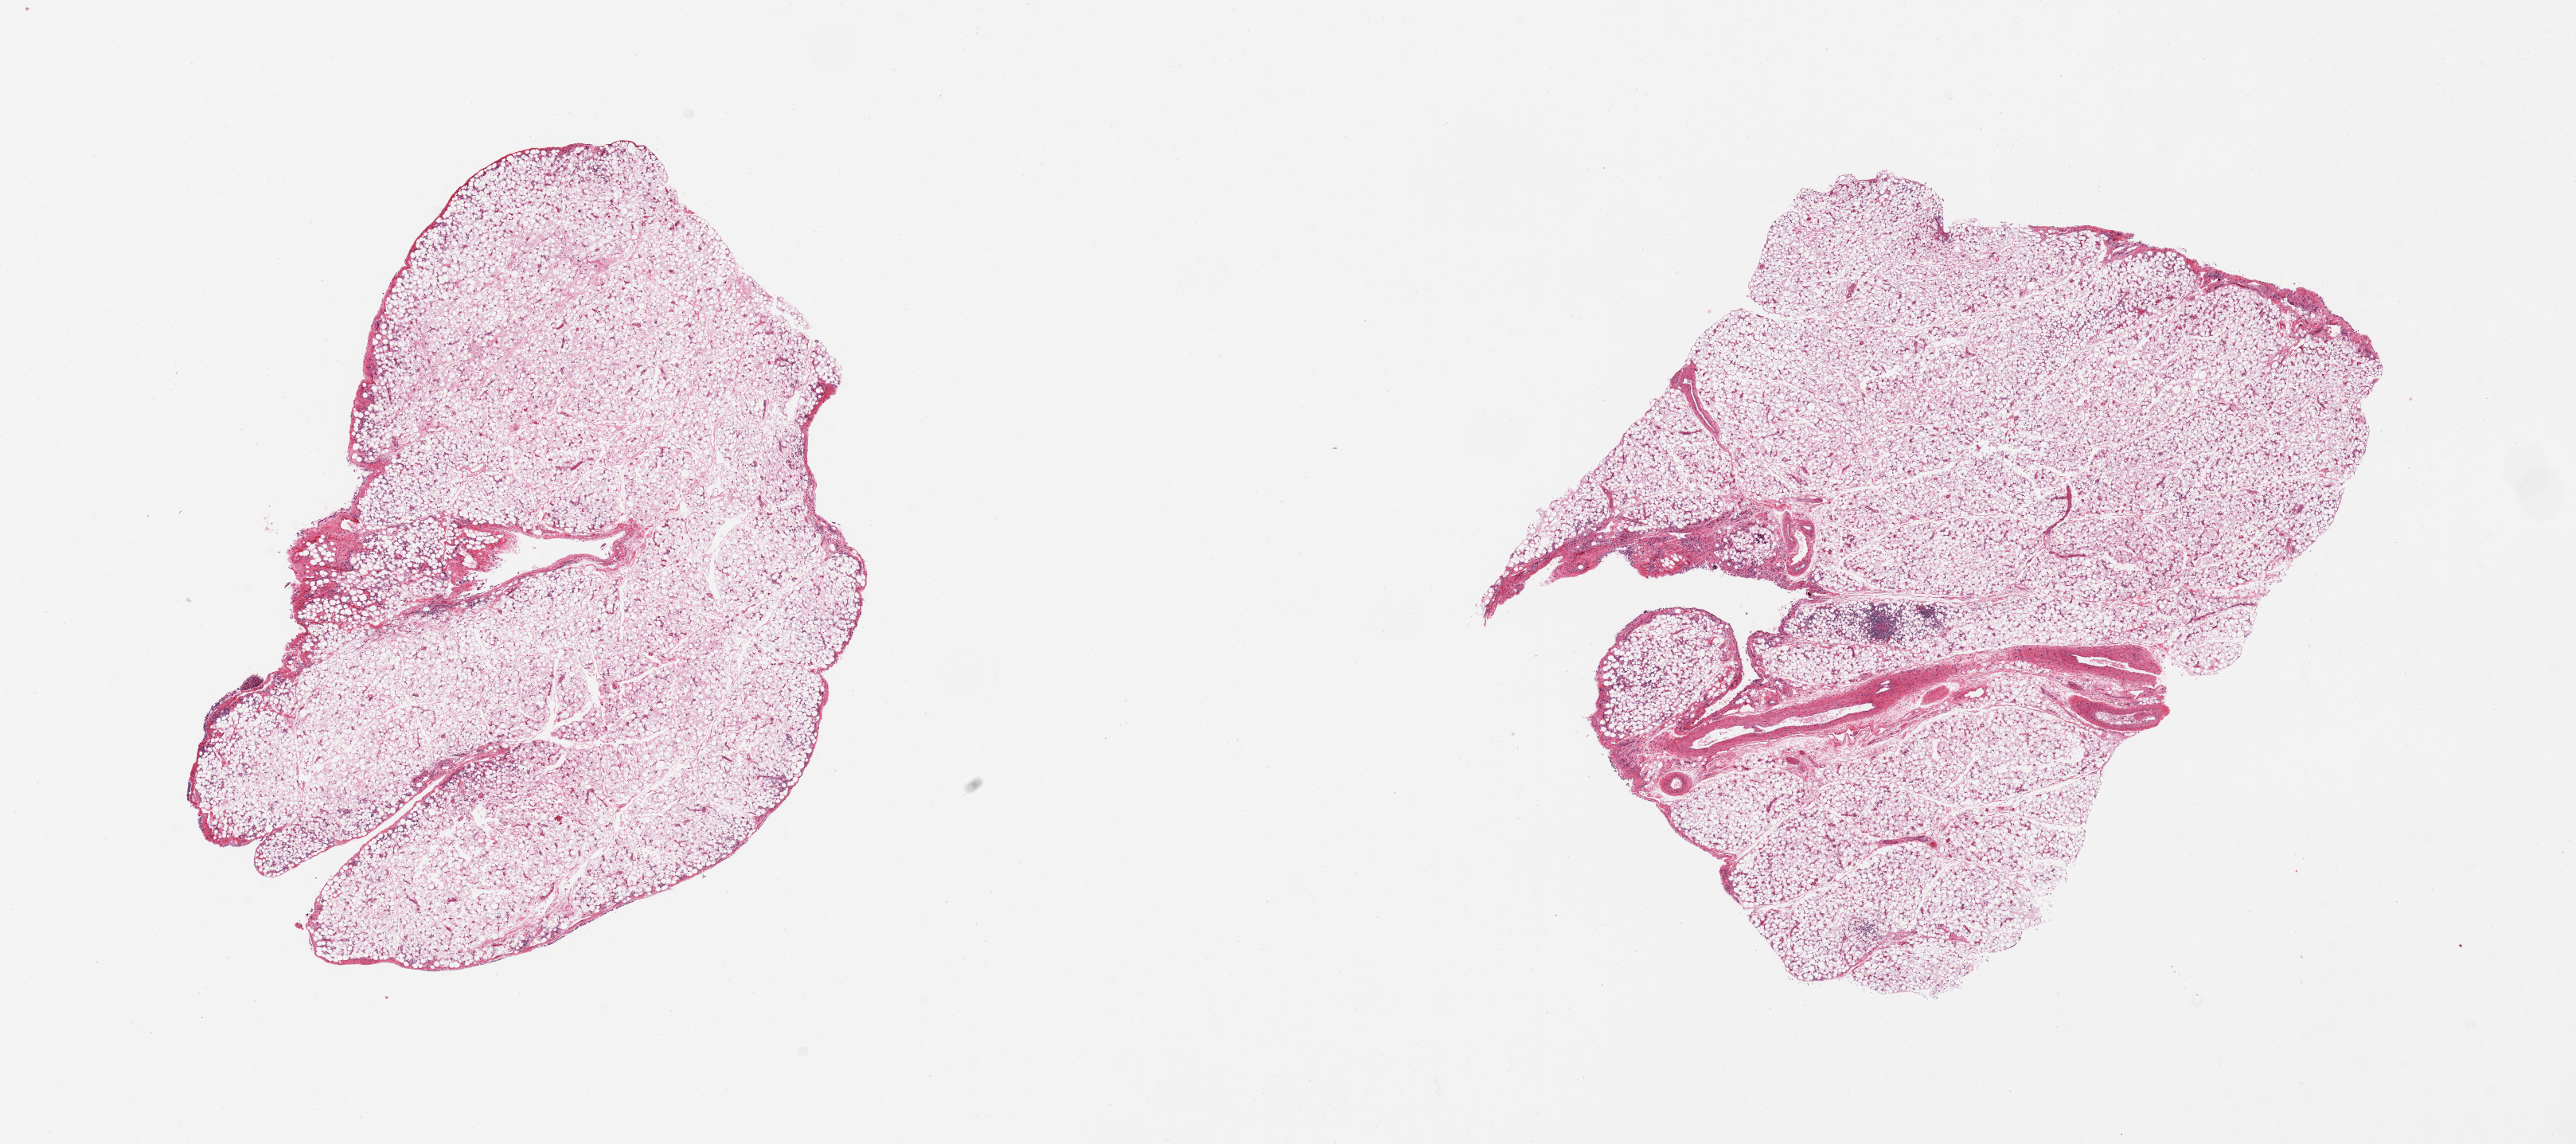
Digitized haematoxylin and eosin-stained section — whole scanned area (about 25.6 x 11.4 mm) shown as a low-resolution overview, PAXgene-fixed paraffin-embedded (PFPE) section, target tissue: omentum, donor tissue sample. Donor: female.
Review note (as recorded): 2 pieces, diffuse mesothelial hyperplasia; ~10% vessel/fibrous tissue.